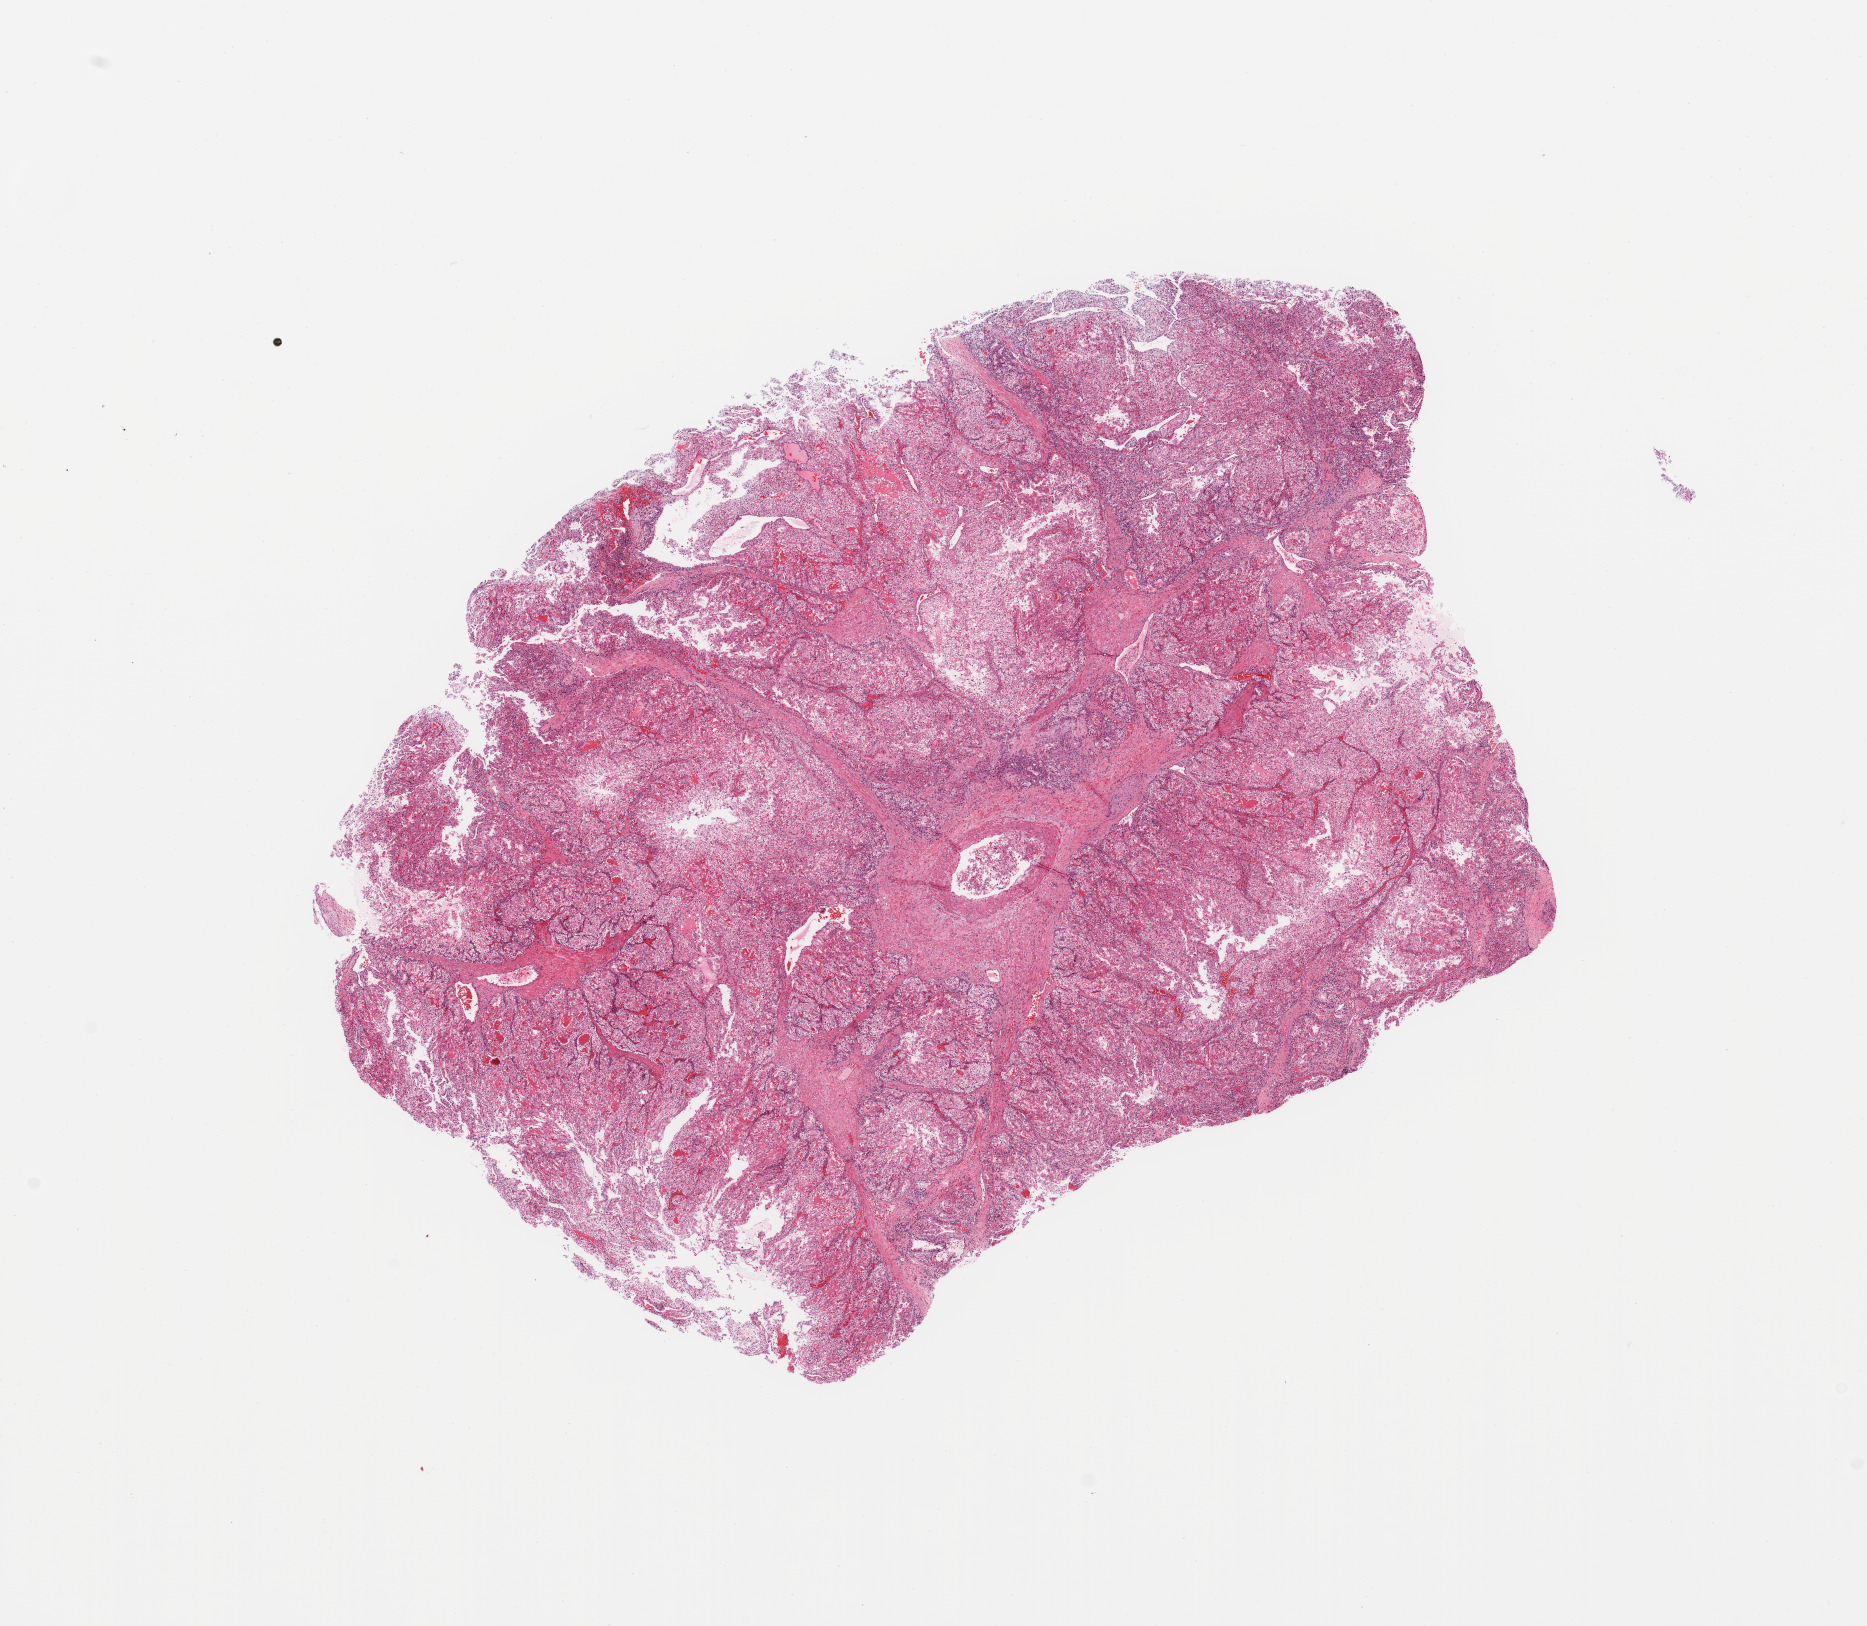
H&E-stained whole-slide image, a low-resolution overview of the entire scanned area, about 14.8 x 12.9 mm, tumour tissue sample, sampled site: kidney. Patient: male, age 52 years. Histologic grade: G2 (moderately differentiated). Pathologist review of this section (percent, as recorded): tumour nuclei 85%, necrosis 5%.
* diagnosis: Renal cell carcinoma, NOS
* AJCC pathologic stage: II